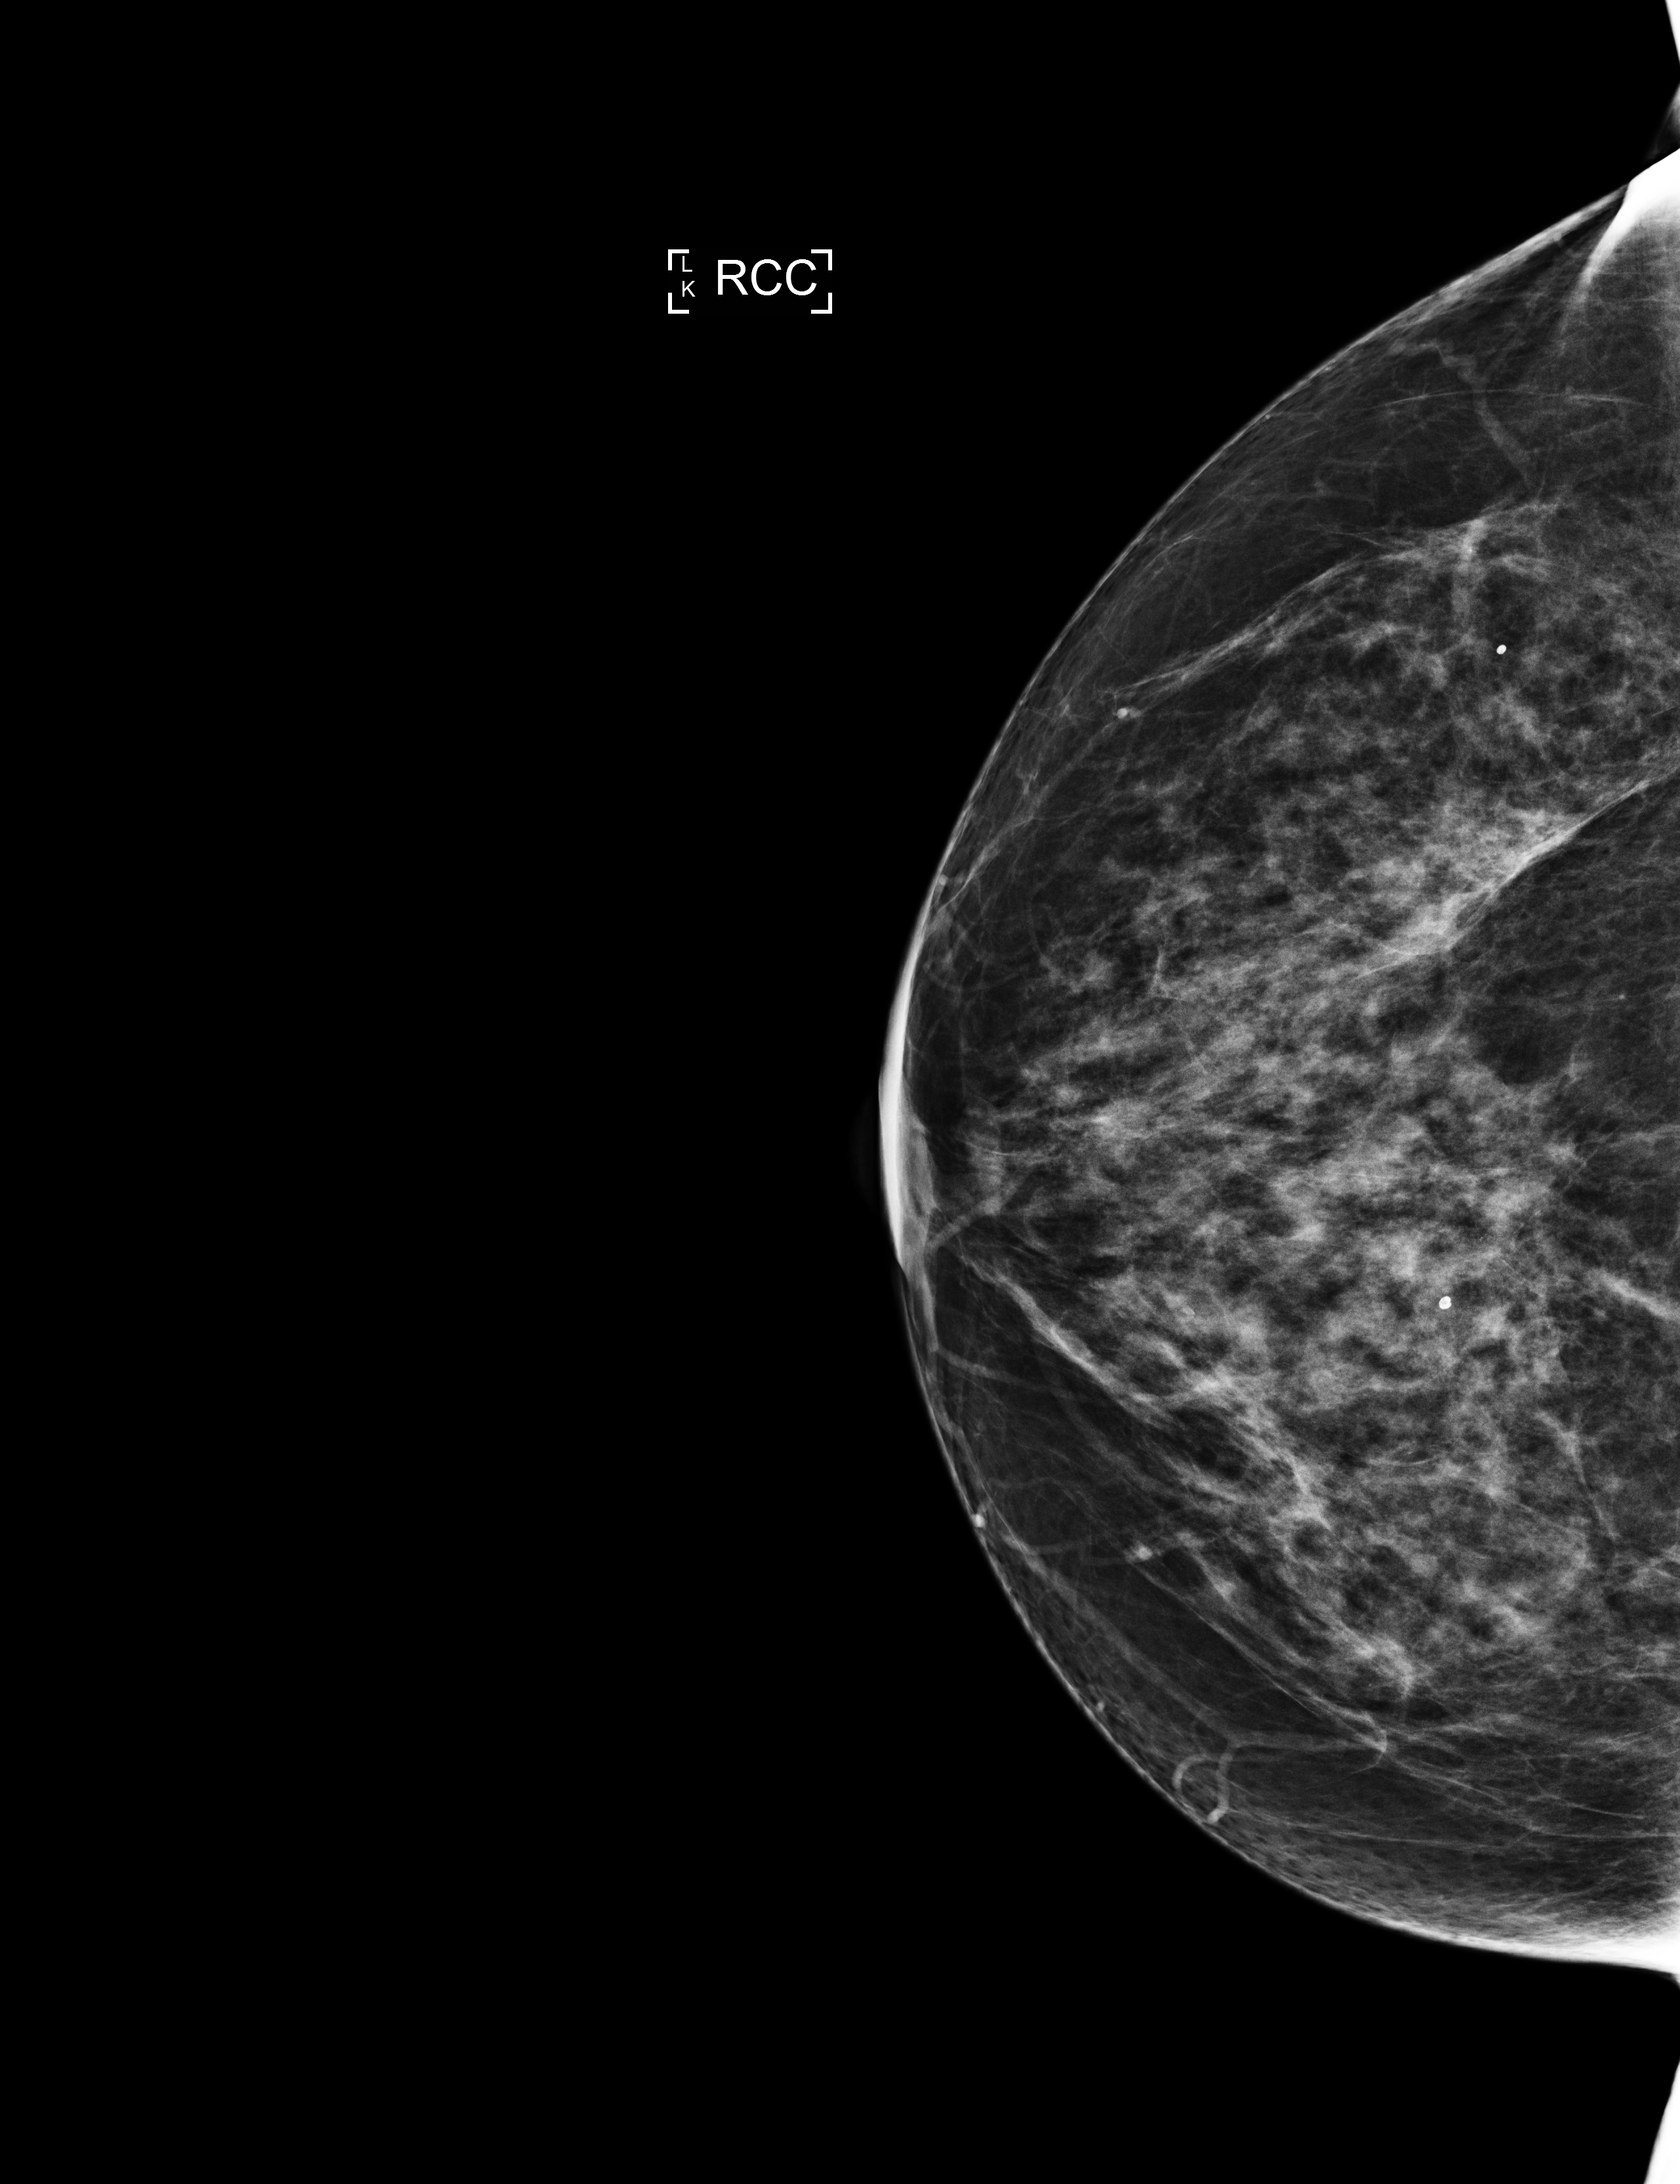
Annual screening mammography examination, compressed breast thickness 71 mm, system: Selenia Dimensions. Patient aged 61 years (female).
Image type: full-field digital mammogram. Breast: right. Projection: cranio-caudal projection.